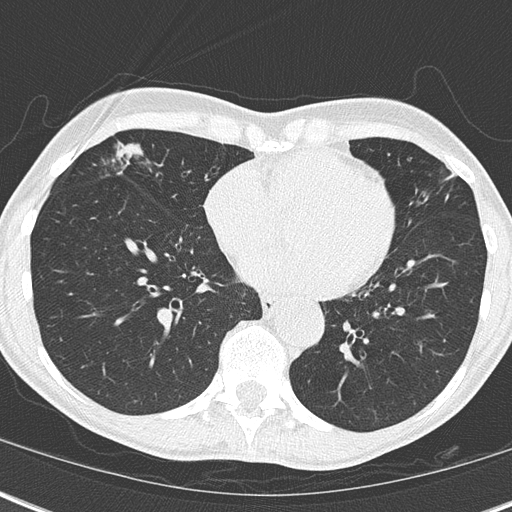
Axial slice from a low-dose chest CT screening exam; third annual screen; lung window (W 1500 / L -600 HU); slice 108 of 173 in the series; 512 × 512 image matrix, field of view 290 × 290 mm. Female participant, aged 67 years at enrolment.
Expert-annotated lung lesion, bounding box [x1, y1, x2, y2] px = [90, 135, 185, 210]. Screening reader's record for this exam (one nodule recorded; not confirmed to be the boxed lesion): non-calcified nodule or mass ≥4 mm, right middle lobe, 32 × 17 mm, mixed attenuation, pre-existing on the prior screen: yes; interval growth: yes. Official screen result: positive, other. Lung cancer was diagnosed 76 days after this screen: bronchiolo-alveolar adenocarcinoma, NOS, right middle lobe, well differentiated (G1), stage IA (AJCC 6th edition), 25 mm at pathology.